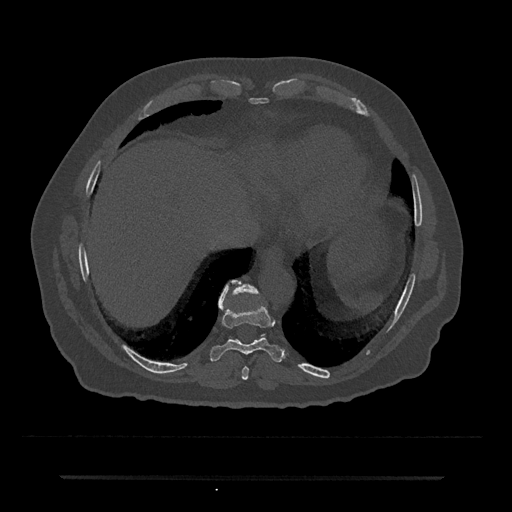
CT including the spine, one axial slice; slice 274 of 797 in the series (ordered by position); 120 kVp; bone window (W 1800 / L 400 HU); 0.5 mm slice thickness; 512 × 512 image matrix, field of view 437 × 437 mm. Patient: male, 69 years. From the clinical record (not read from this slice): primary cancer: prostate.
Outlined on this slice (semi-automatically segmented with operator editing):
- T10 vertebra: bounding box [x1, y1, x2, y2] px = [227, 281, 259, 312]
- T8 vertebra: [242, 366, 249, 380]
- T9 vertebra: [209, 280, 285, 362]